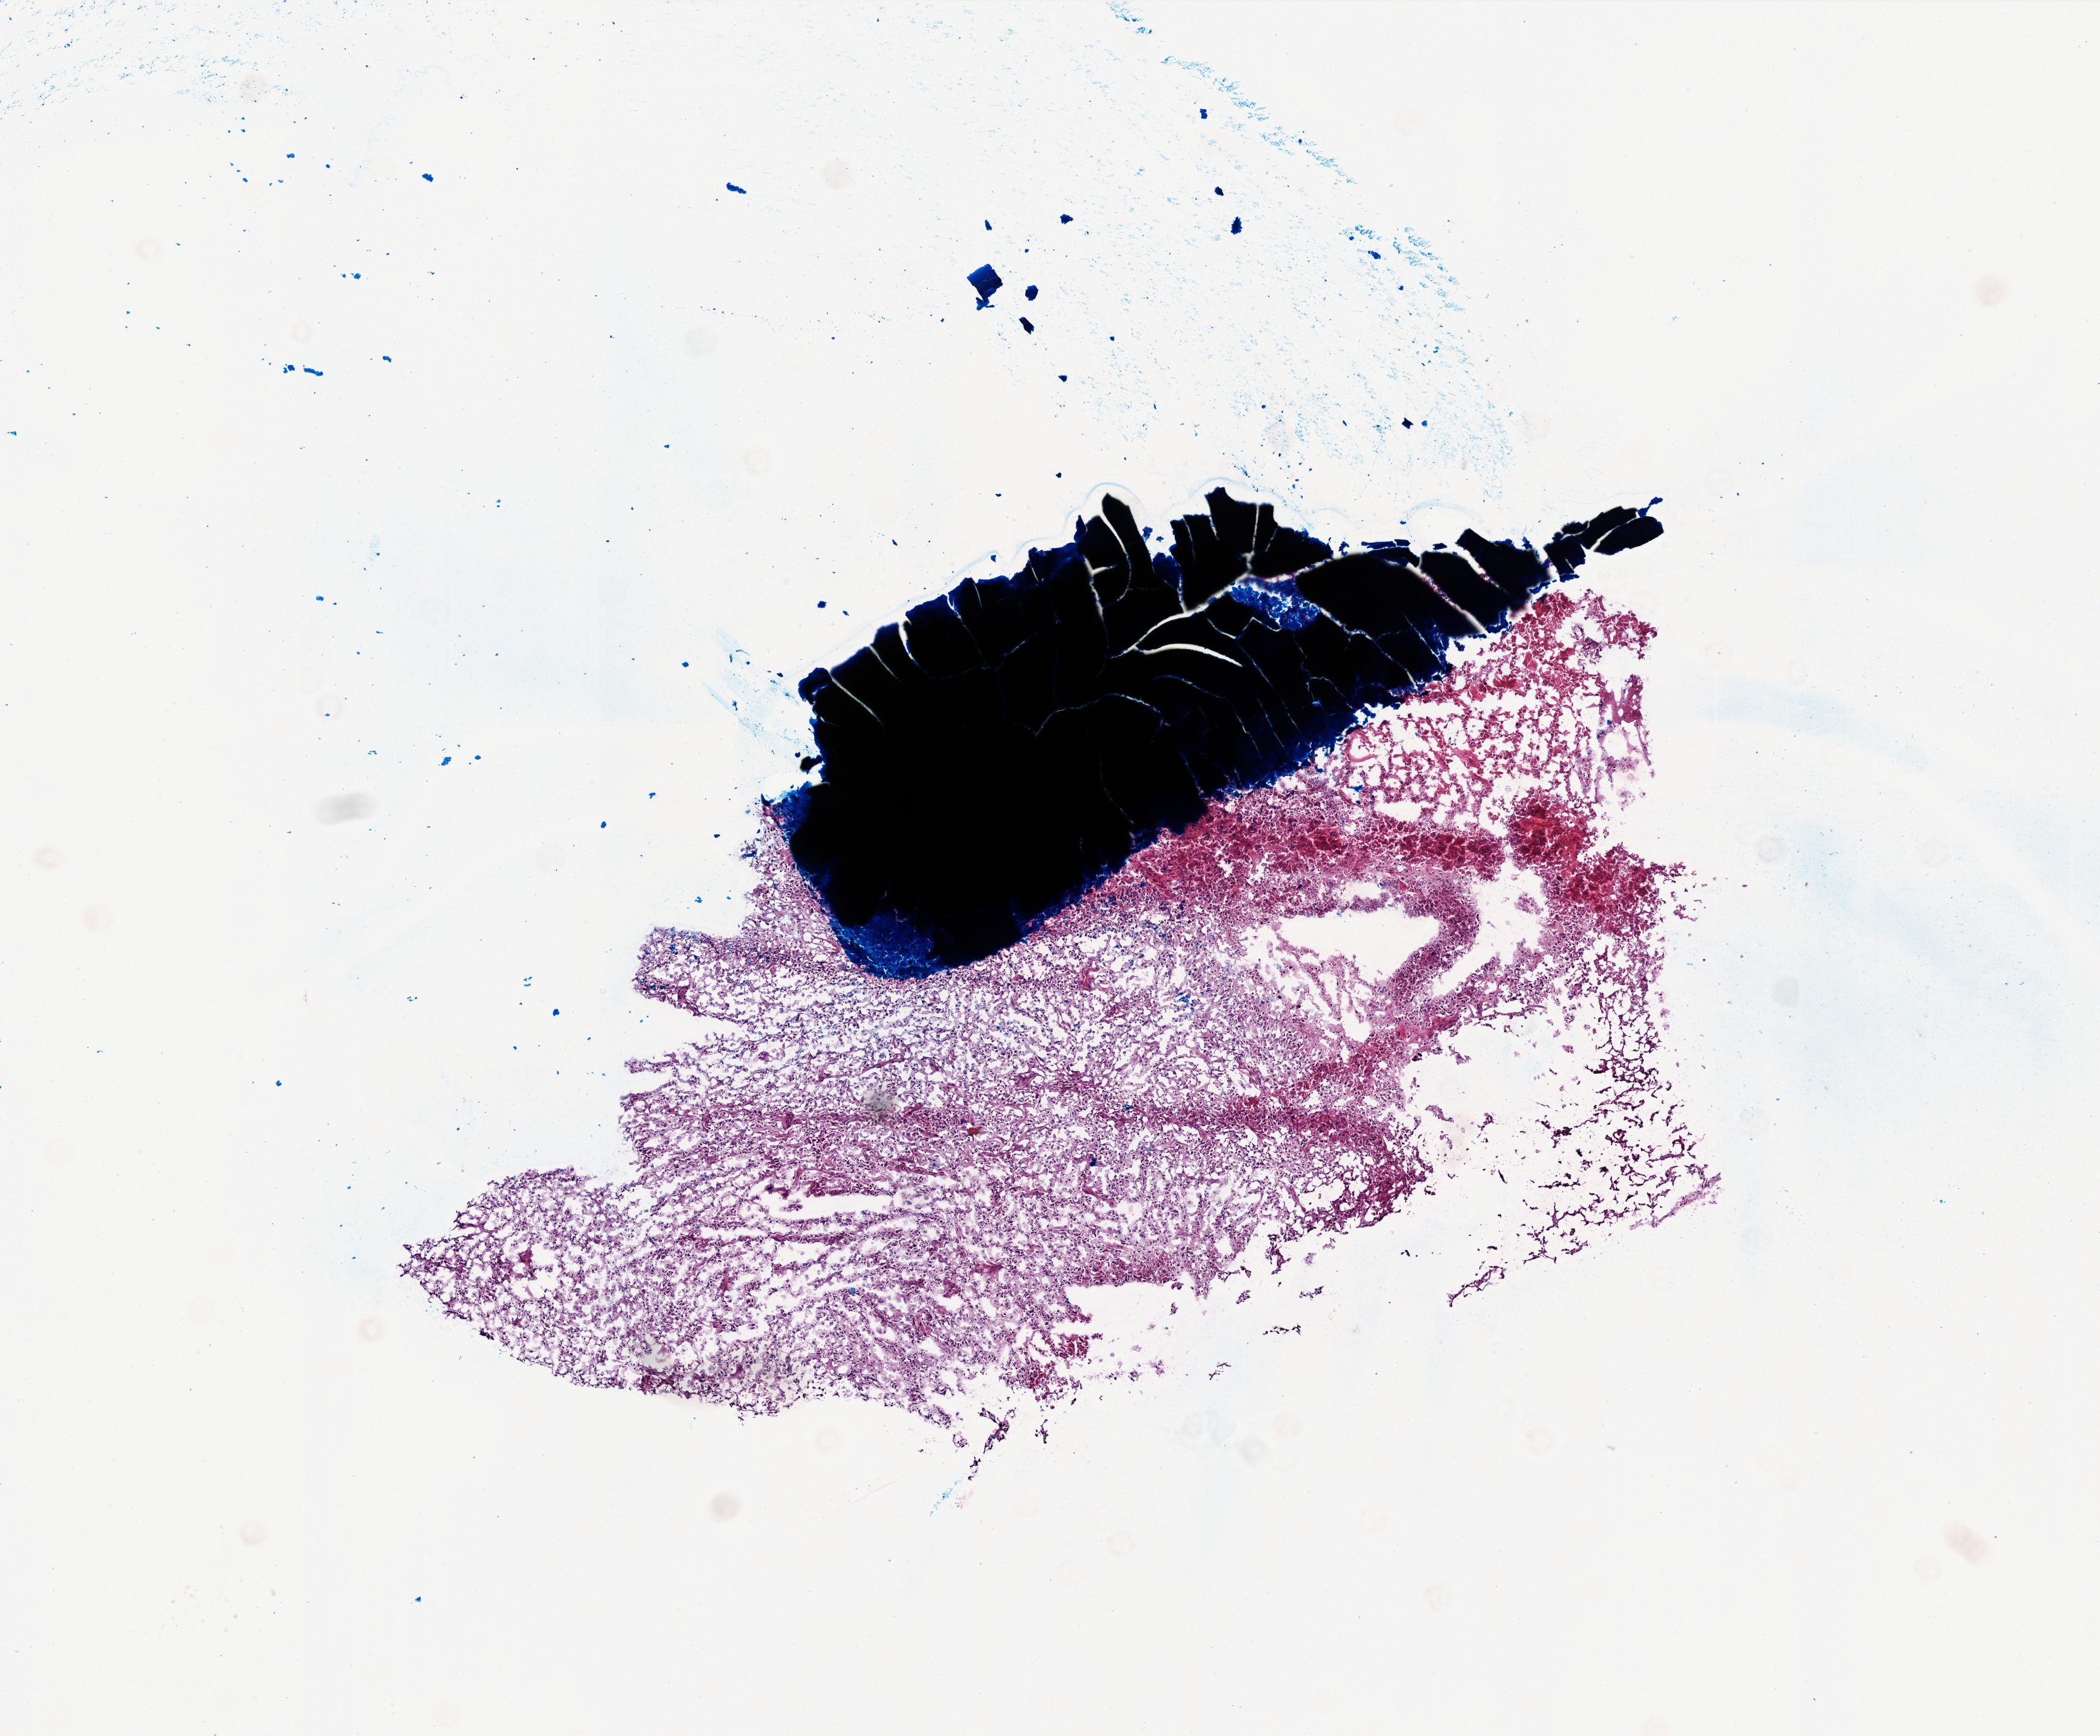
Digitized Hematoxylin and eosin (H&E) stained tissue section (whole slide) — a low-resolution overview of the entire scanned area, about 7.0 x 5.8 mm; frozen section; brain, primary tumour sample. Male patient; age at initial diagnosis 51 years. Pathologist review of this section (percent, as recorded): tumour cells 90%, tumour nuclei 90%, normal cells 0%, stromal cells 5%, necrosis 5%.
- pathologic diagnosis: Glioblastoma